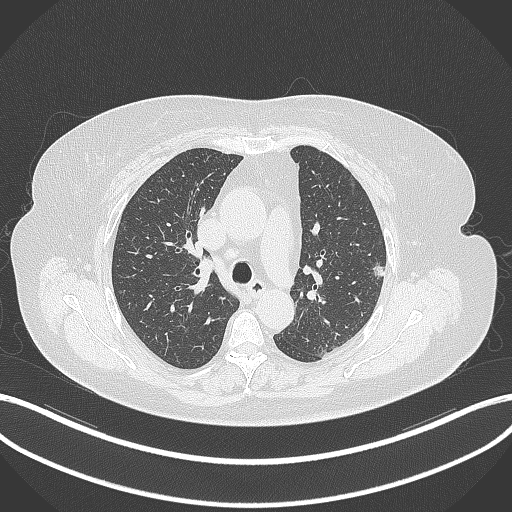
Chest CT, one axial slice; slice 216 of 309 in the series (ordered by position); reconstruction kernel B70f; 120 kVp; lung window (W 1500 / L -600 HU); 1 mm slice thickness; 512 × 512 image matrix, field of view 400 × 400 mm. Female patient, age 70 years. From the clinical record (not read from this slice): clinical TNM (as recorded): T1c N0 M0.
Outlined on this slice (rectangle marked by the reading radiologist):
- lung tumour (recorded histology: adenocarcinoma): bounding box [x1, y1, x2, y2] px = [366, 263, 383, 280]